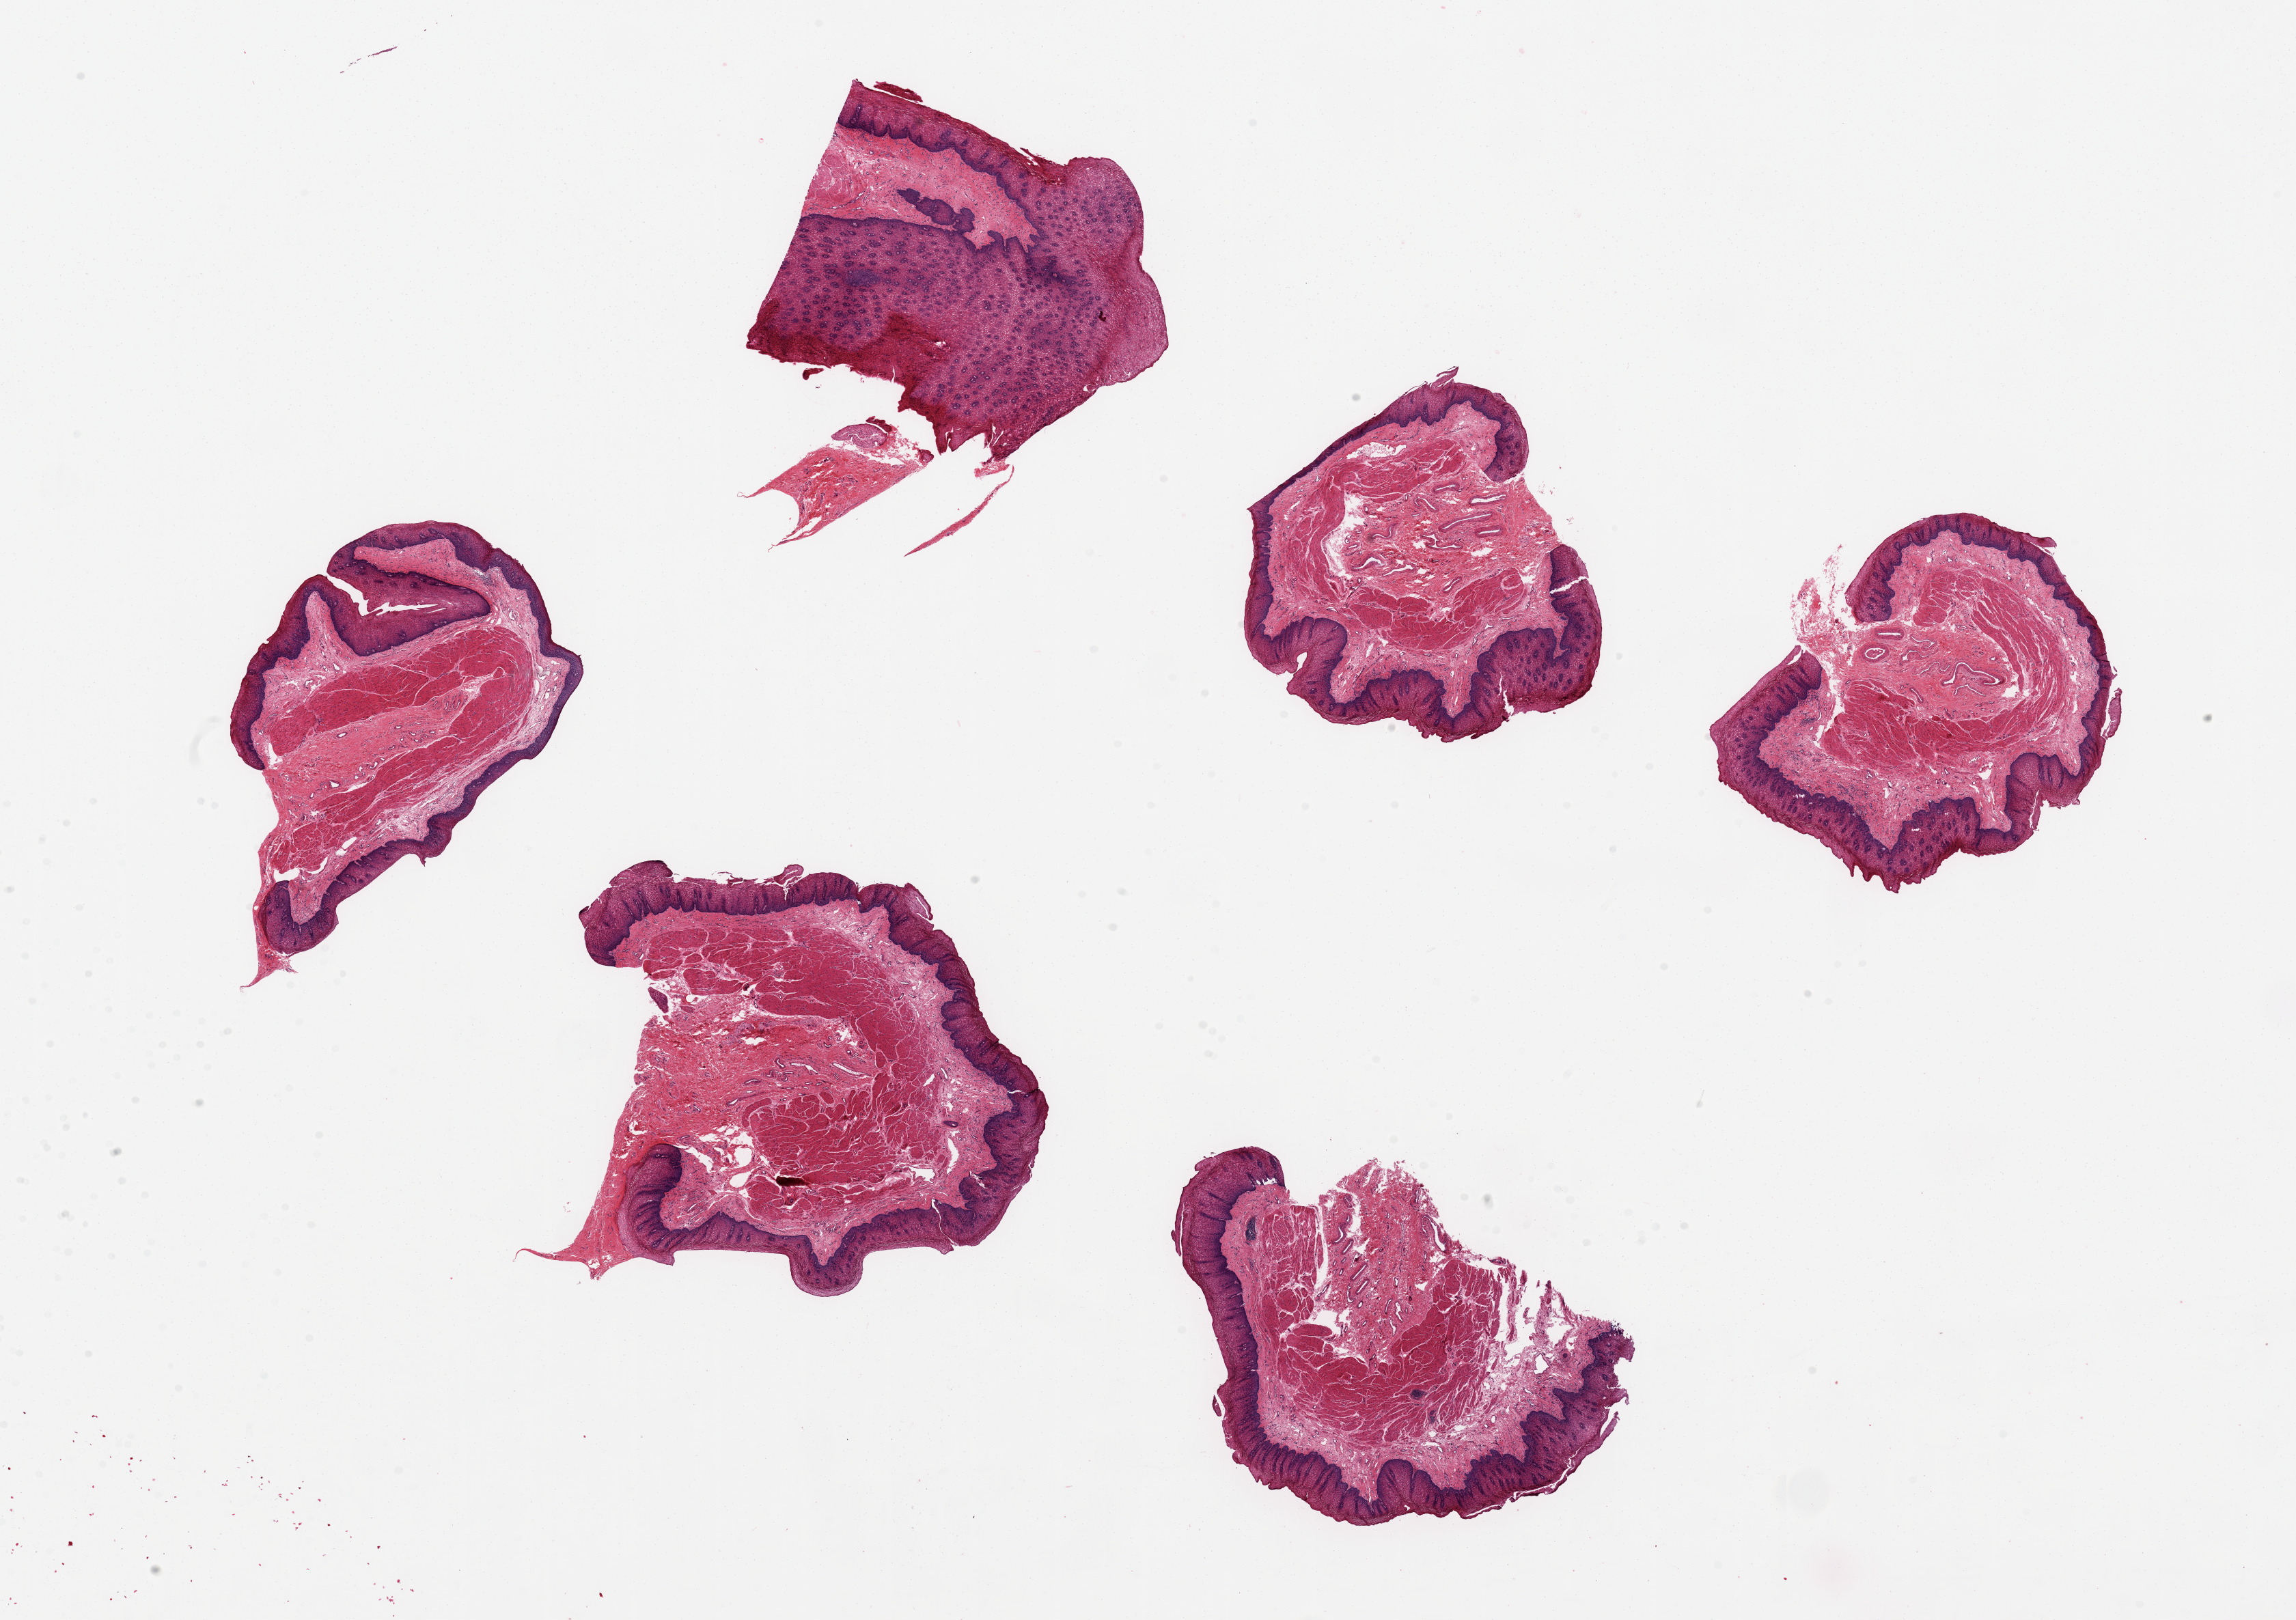
Whole-slide image, H&E stain, brightfield — a low-resolution overview of the entire scanned area, about 26.6 x 18.8 mm. PAXgene-fixed, paraffin-embedded tissue. Target tissue: esophageal mucous membrane. Tissue donor sample.
Review note (as recorded): 6 pieces,~5 mm sq with well preserved epithelium (0.25 mm thick).